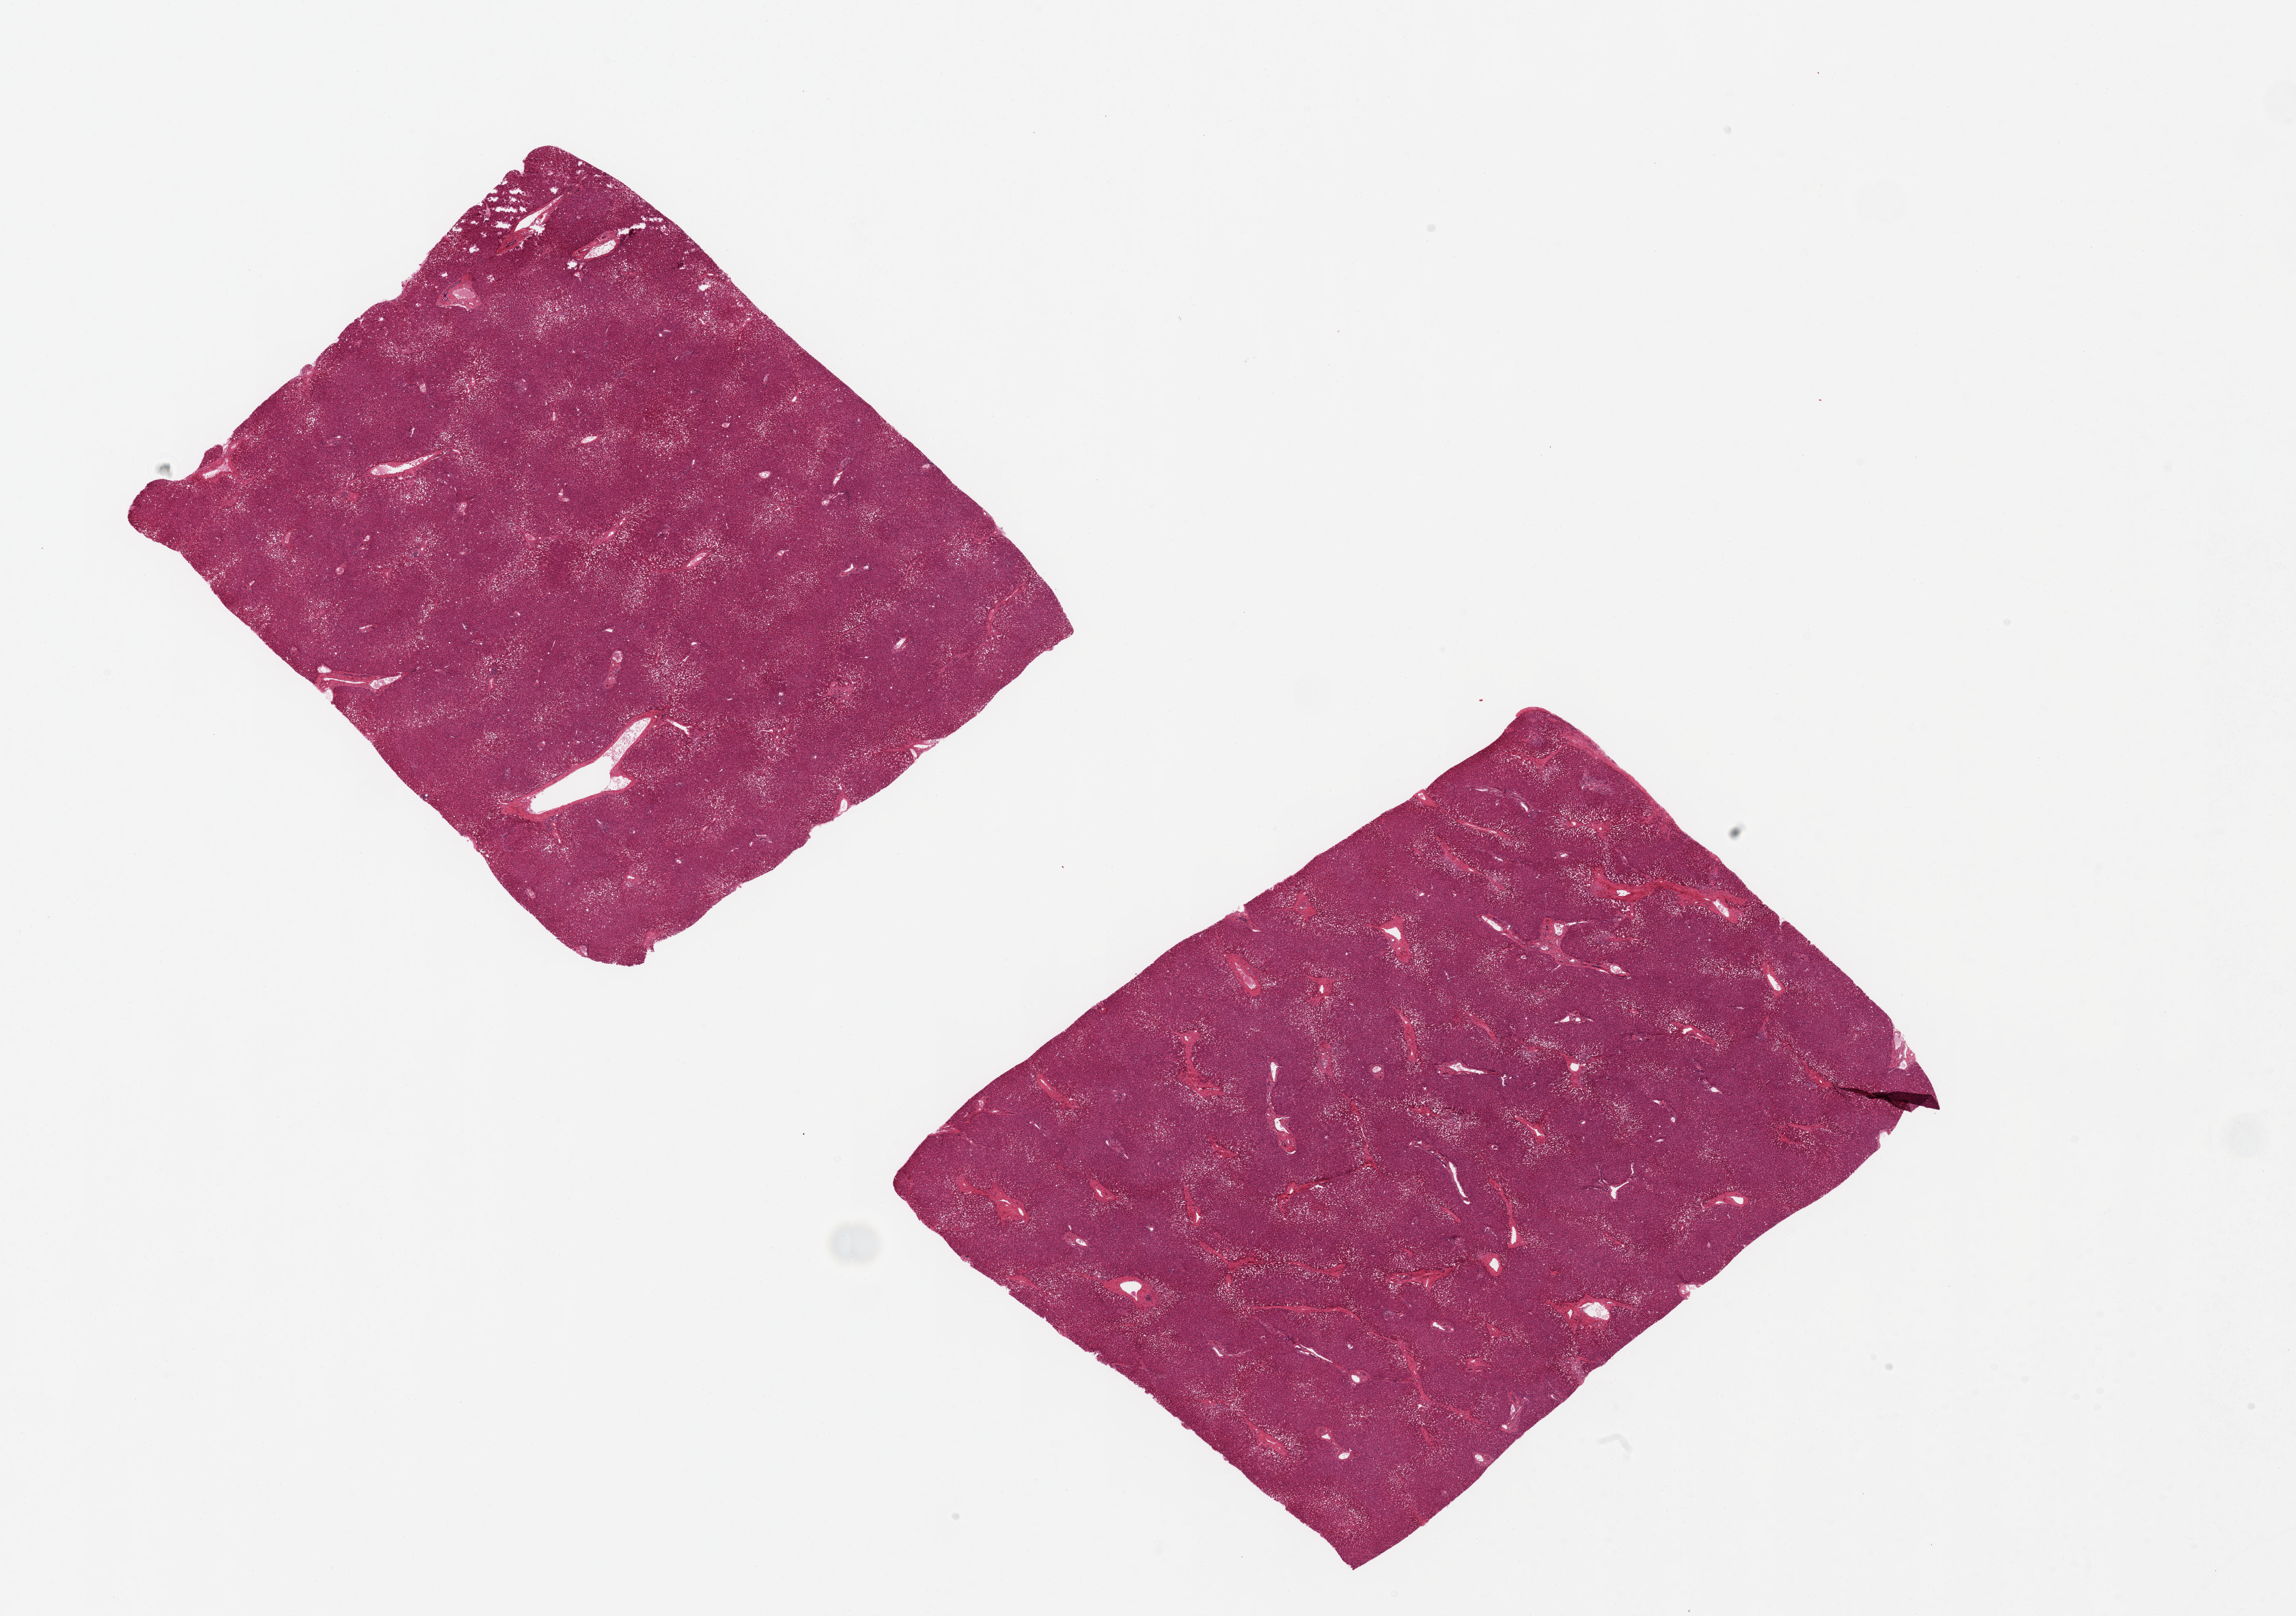
Whole-slide image, haematoxylin and eosin stain, a low-resolution overview of the entire scanned area, about 26.6 x 18.7 mm. PAXgene-fixed, paraffin-embedded tissue. Section of liver (target tissue). Donor tissue sample. Donor: female.
Review note (as recorded): 2 pieces, 9x7 & 8x7 mm; moderate macrovesicular steatosis; no fibrosis.